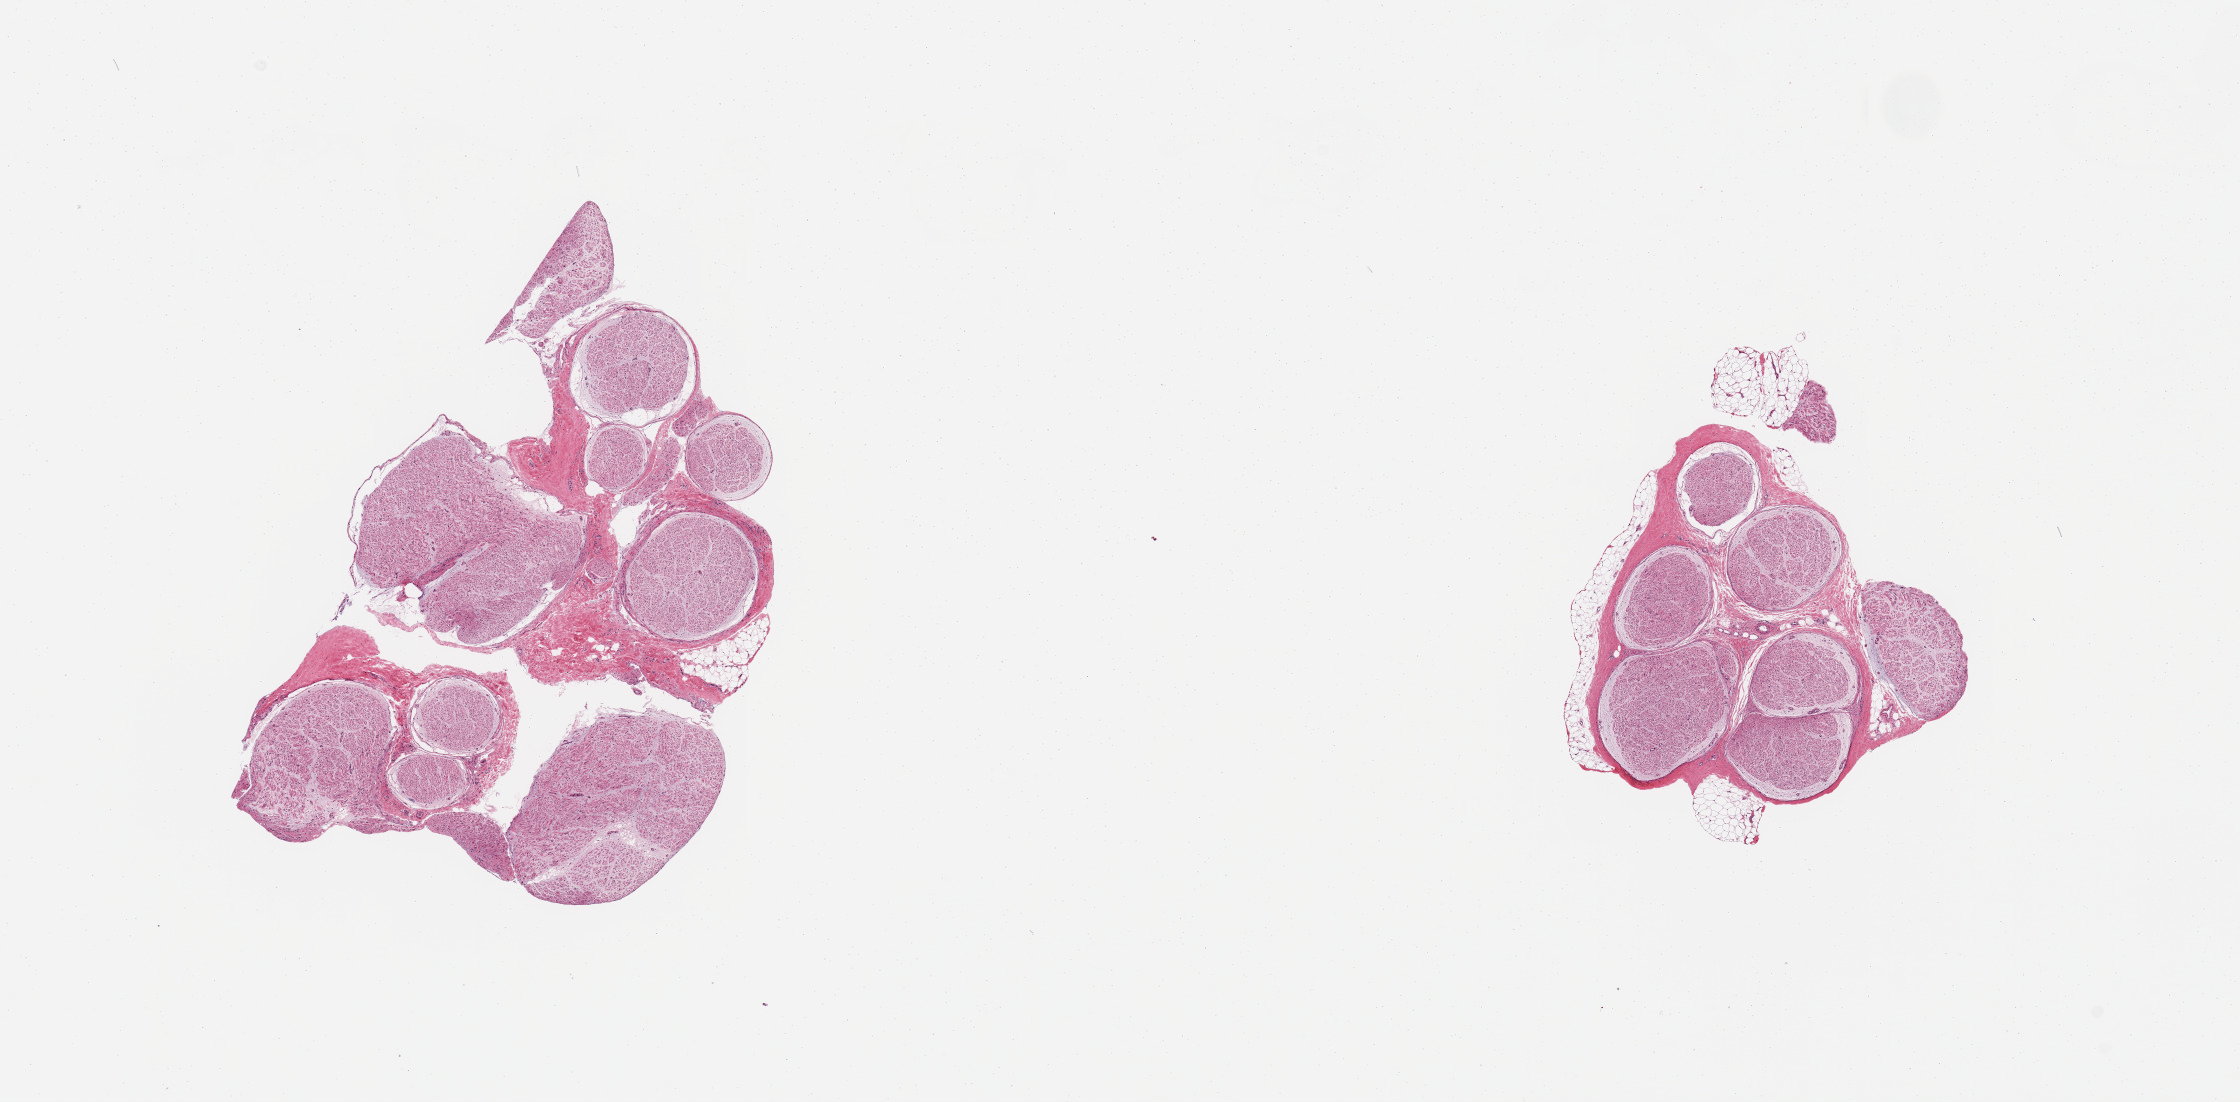
Whole-slide image, hematoxylin and eosin (H&E) stain — shown as a low-resolution overview of the whole scanned area (about 17.7 x 8.7 mm, slide scanned at 20x). PAXgene-fixed paraffin-embedded (PFPE) section. Sampled site (target tissue): tibial nerve. Tissue donor sample. Donor: female.
Review note (as recorded): 2 pieces; thin band of external fat around 1 piece [0.2mm thick].